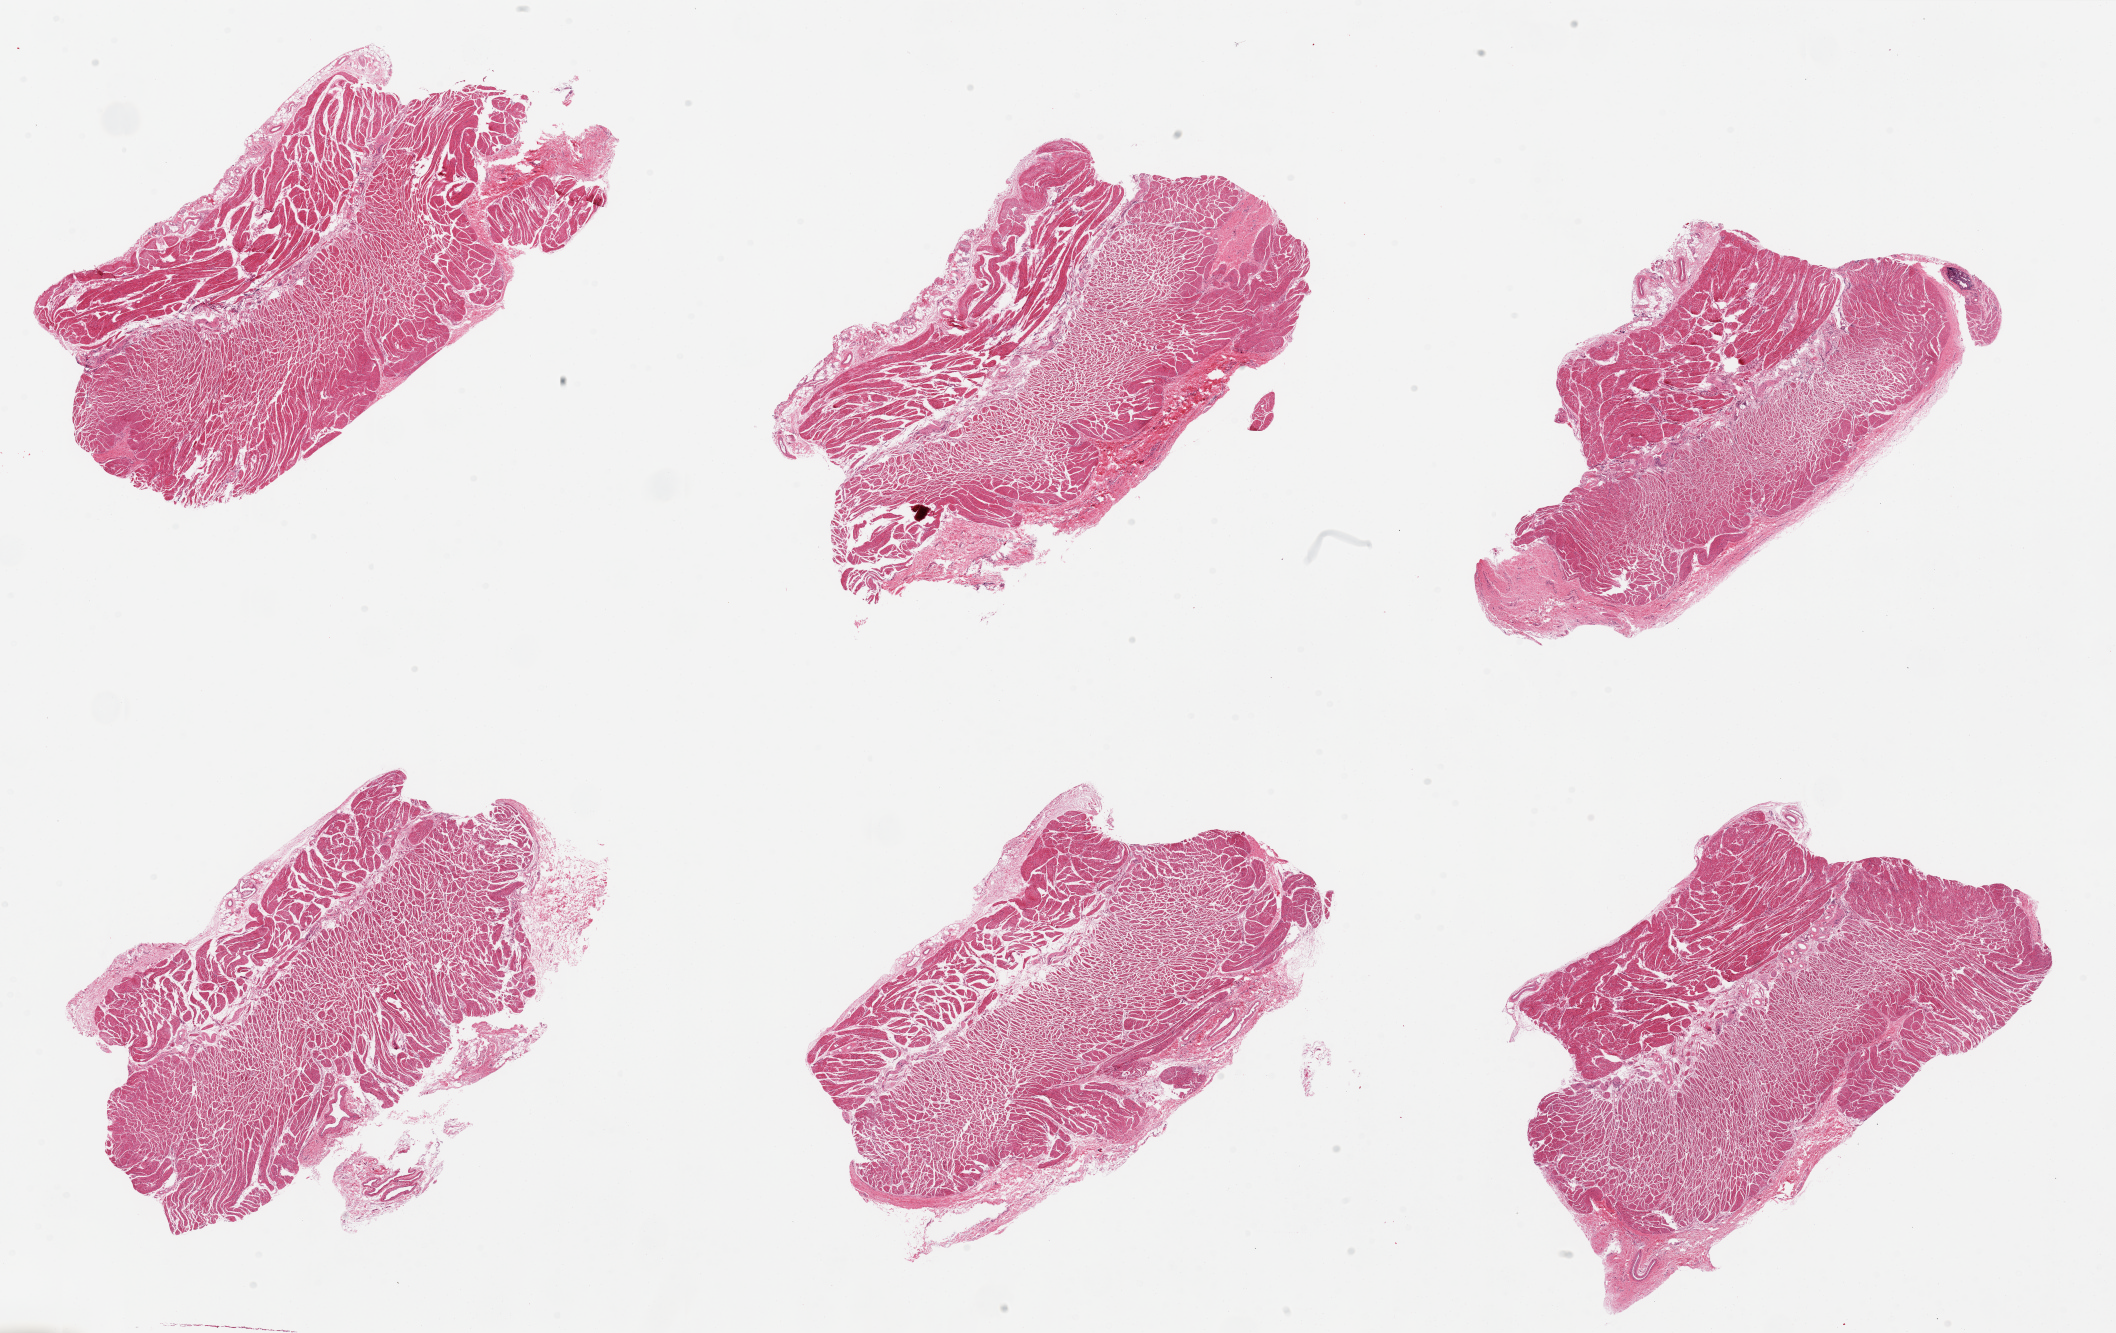
Hematoxylin and eosin (H&E) whole-slide image, shown as a low-resolution overview of the whole scanned area (about 33.5 x 21.1 mm, from a 20x scan). PAXgene-fixed paraffin-embedded (PFPE) section. Sampled site (target tissue): esophageal muscle. Tissue donor sample. Male donor.
- review note (as recorded): 6 pieces, well trimmed